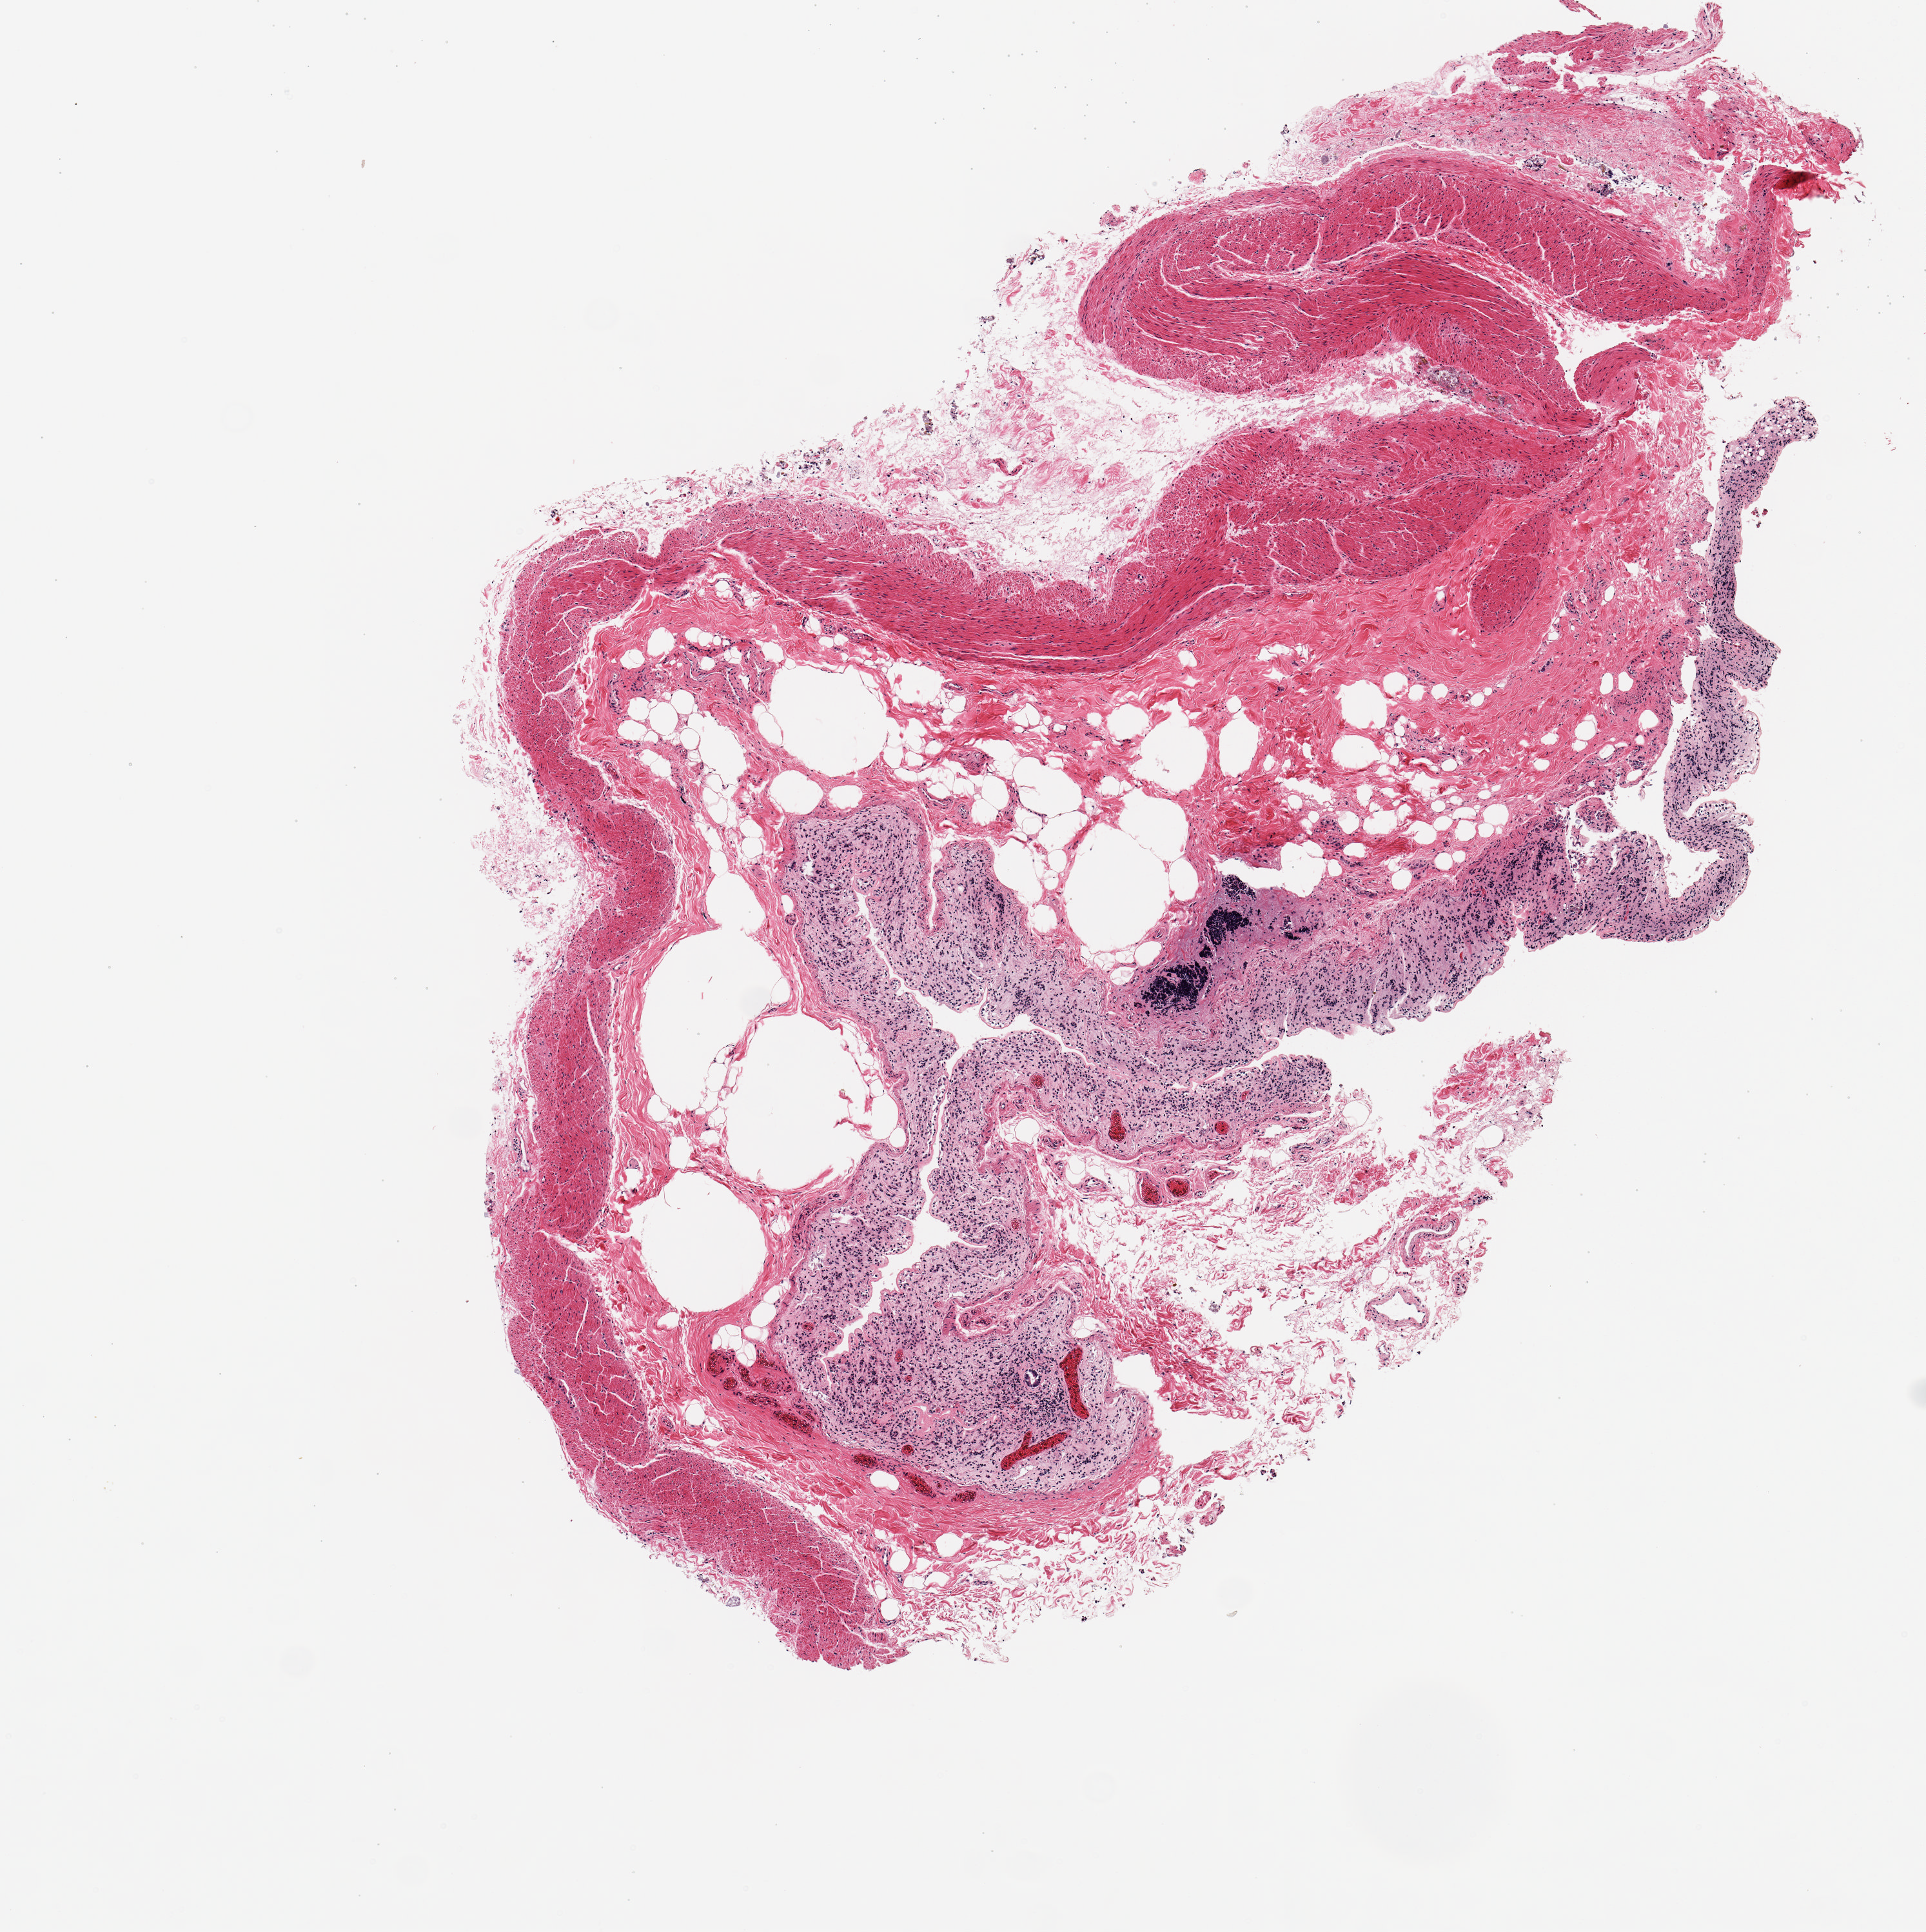
Digitized hematoxylin and eosin (H&E)-stained section — shown as a low-resolution overview of the whole scanned area (about 5.9 x 5.9 mm); PAXgene-fixed, paraffin-embedded tissue; target tissue: transverse colon; tissue donor sample. Donor sex: male.
- pathologist's review note for this sample: 1 pieces; full thickness section with mucosal autolysis